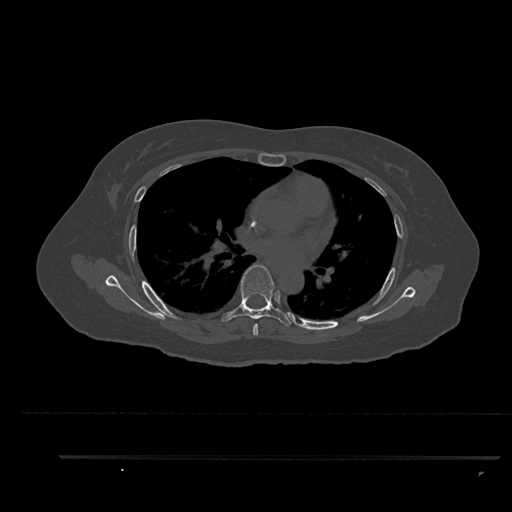
CT including the spine, one axial slice; position 564 of 797 along the scan axis; reconstruction kernel Br40s/3; 120 kVp; bone window (W 1800 / L 400 HU); 0.5 mm slice thickness; 512 × 512 image matrix, field of view 408 × 408 mm. Female patient, age 44 years. From the clinical record (not read from this slice): primary cancer: renal.
Structures marked on this image (semi-automatically segmented with operator editing):
- T5 vertebra: bounding box [x1, y1, x2, y2] px = [253, 324, 258, 335]
- T6 vertebra: [222, 264, 296, 326]